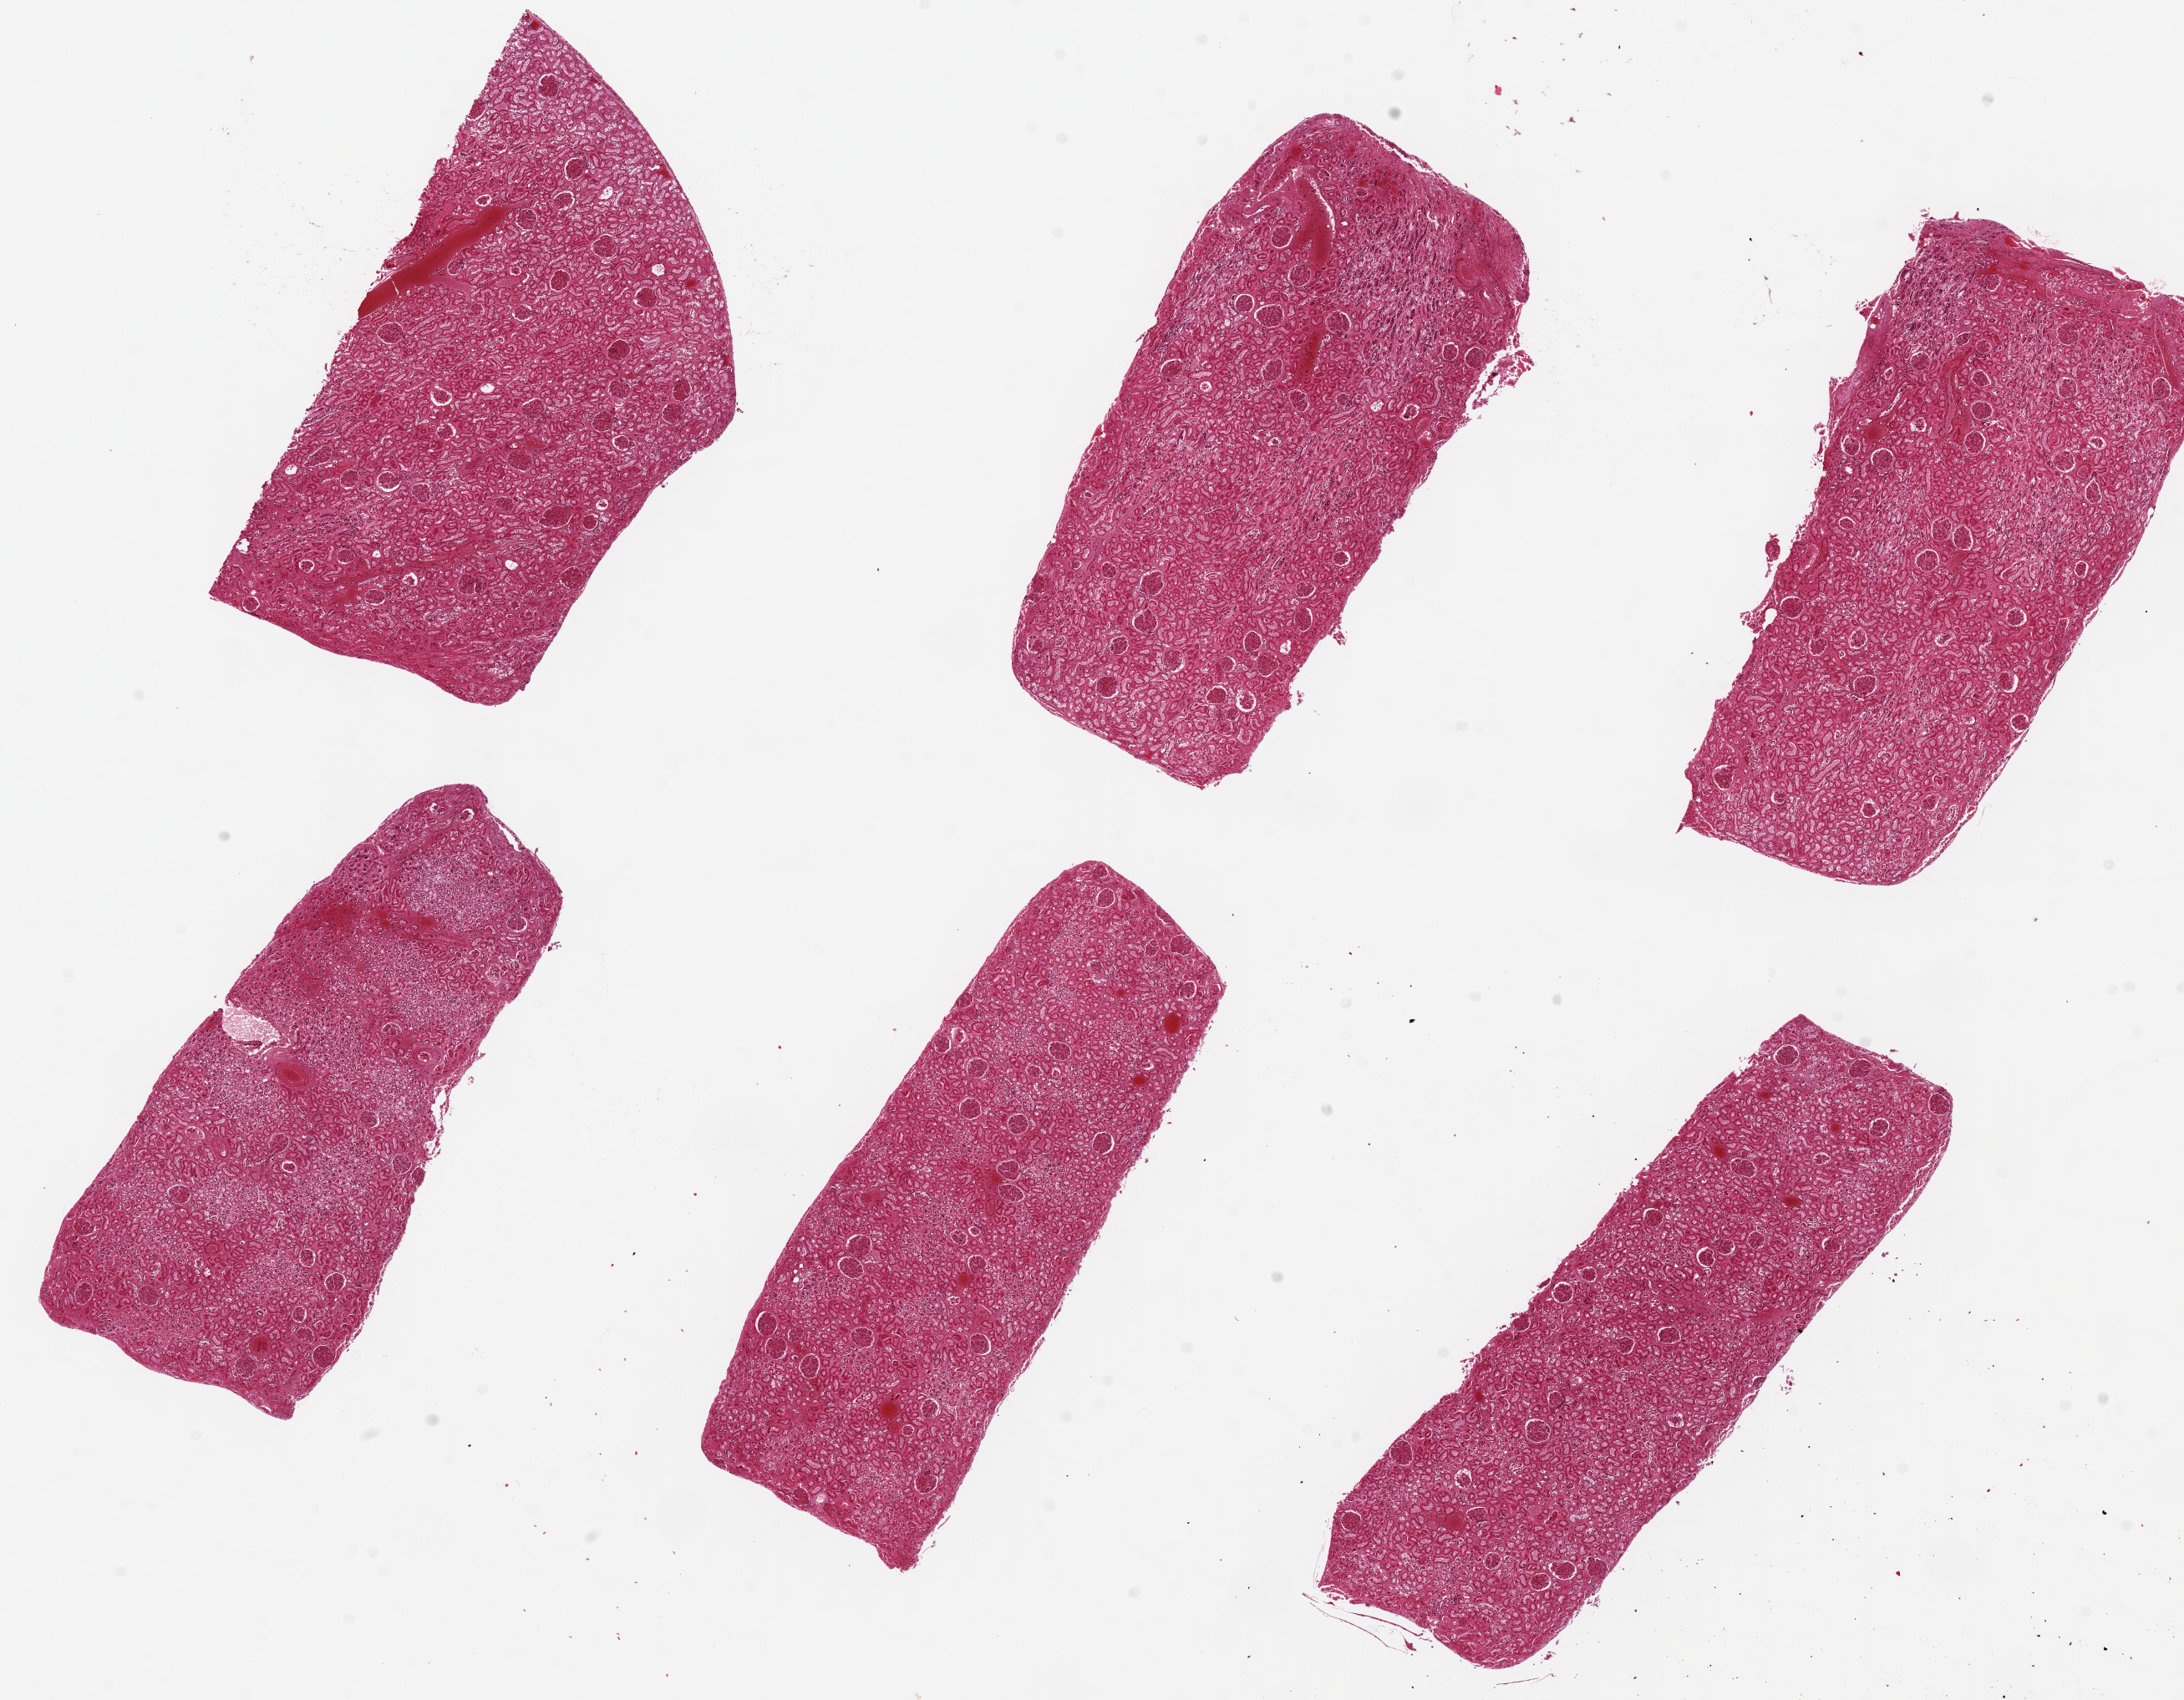
Whole-slide image, haematoxylin and eosin stain, shown as a low-resolution overview of the whole scanned area (about 20.7 x 16.1 mm, from a 20x scan). PAXgene-fixed paraffin-embedded (PFPE) section. Sampled site (target tissue): renal cortex. Donor tissue sample. Male donor.
• pathologist's review note for this sample: 6 pieces ~6x3mm, badly autolyzed